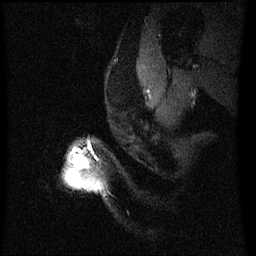
Breast MRI (dynamic contrast-enhanced), one sagittal slice. Position 52 of 60 along the scan axis. Dynamic contrast-enhanced series, image 2 of 3 at this slice position (ordered by acquisition). 1.5 T. TE 4.2 ms, TR 8 ms. 2.2 mm slice thickness. 256 × 256 image matrix, field of view 200 × 200 mm. Female patient, age 50 years.
Annotated regions visible in this slice (semi-automatic segmentation, software-assisted and operator-edited):
- analysis volume of interest (the breast-tissue region the enhancement analysis was run in; not a lesion): bounding box [x1, y1, x2, y2] px = [71, 158, 79, 169]
- tumour enhancement mask (voxels above the 70 % enhancement threshold inside the analysis volume of interest): [75, 160, 78, 163]